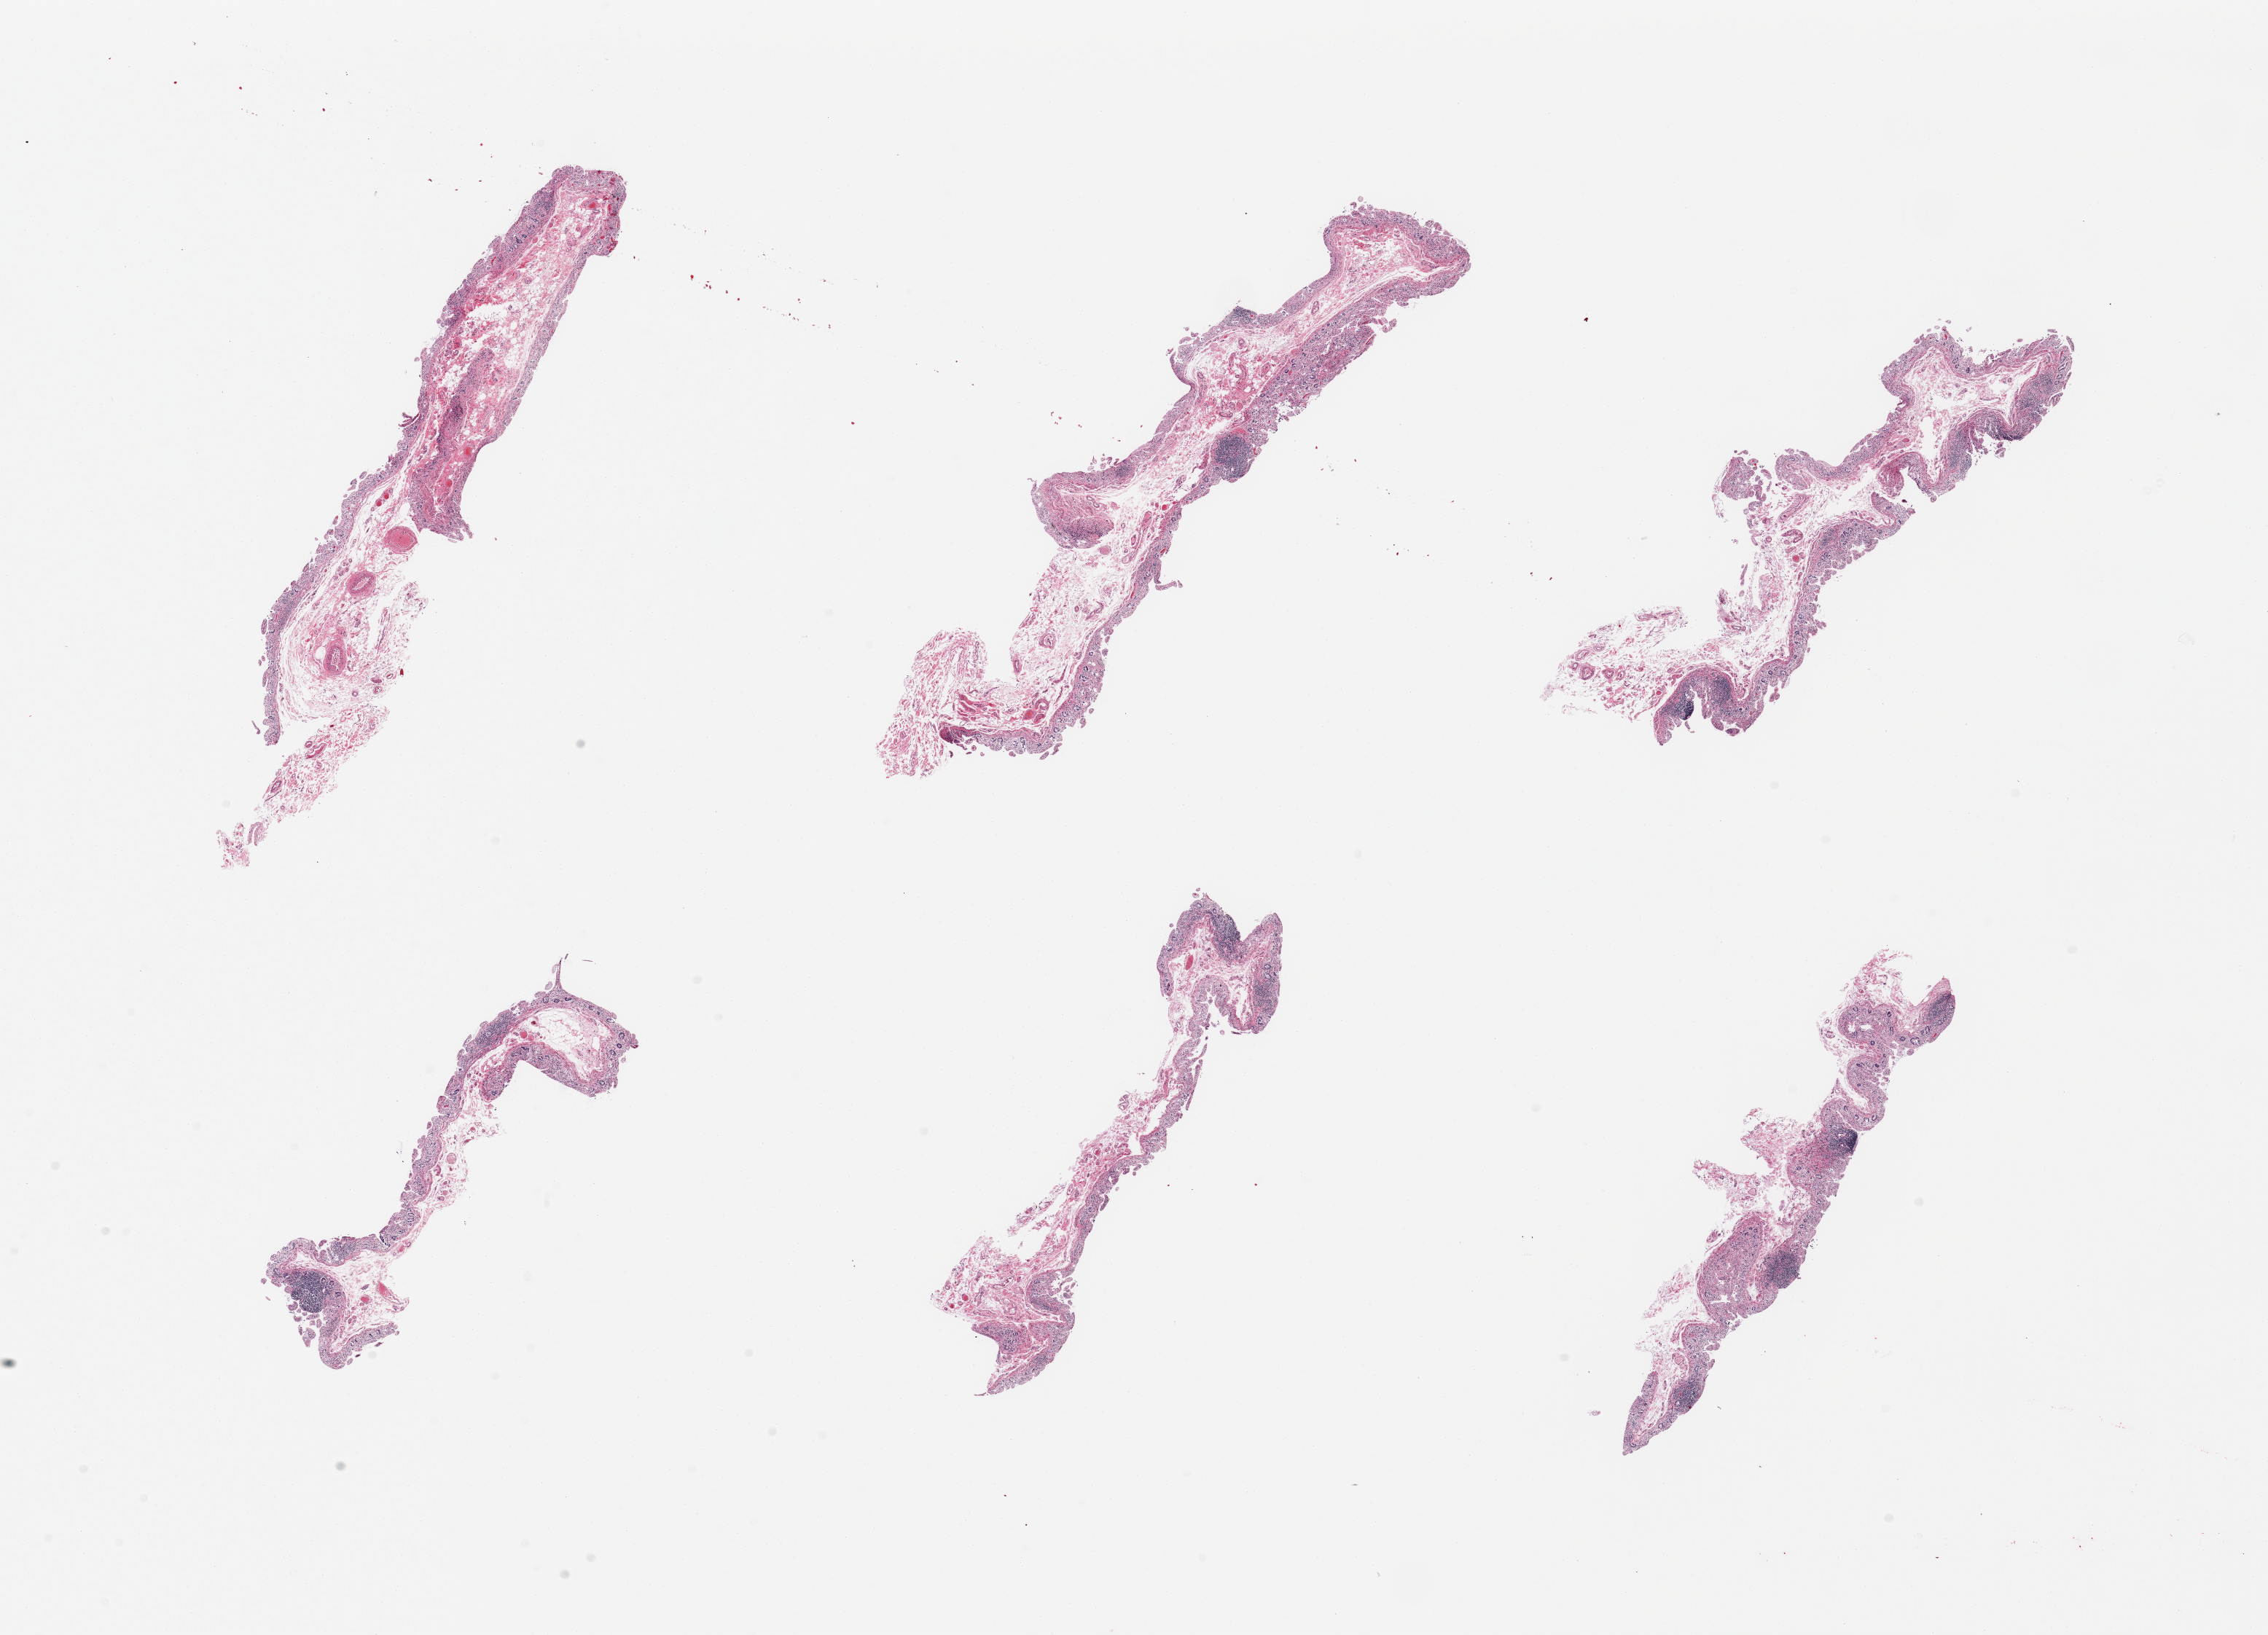
Digitized haematoxylin and eosin-stained section, brightfield — a low-resolution overview of the entire scanned area, about 24.6 x 17.7 mm (slide scanned at 20x). PAXgene-fixed, paraffin-embedded tissue. Section of ileum (target tissue). Donor tissue sample. Male donor.
Review note (as recorded): 6 pieces; largely autolyzed mucosa/submucosa with only scattered lymphoid component, too minimal to warrant analysis.